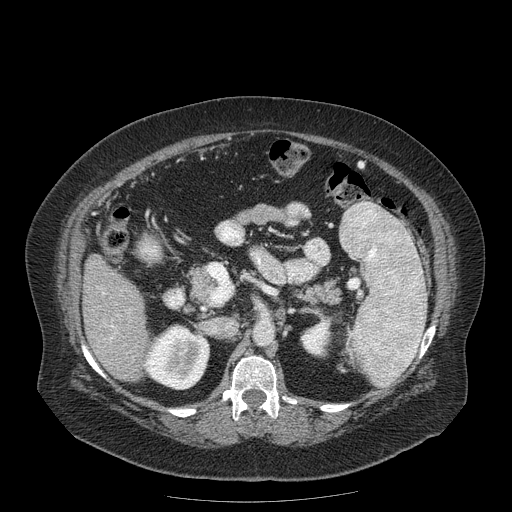
Contrast-enhanced abdominal CT (liver protocol), one axial slice; slice 75 of 204 in the series (ordered by position); reconstruction kernel STANDARD; soft-tissue window (W 400 / L 40 HU); 2.5 mm slice thickness; 512 × 512 image matrix, field of view 440 × 440 mm. Case-level facts recorded for this patient, not image findings: diagnosis: hepatocellular carcinoma (patient treated with transarterial chemoembolisation; whether this scan precedes or follows treatment is not stated here); TNM stage (as recorded): Stage-IIIB; Child-Pugh class: A; tumour differentiation: well differentiated.
Annotated regions visible in this slice (semi-automatically segmented with operator editing):
- liver parenchyma outside the tumour (the mass and vessels are separate outlines, so this box may not span the whole liver): box from (x=82, y=255) to (x=148, y=380) px
- liver vessels: (x=103, y=293)–(x=113, y=340)